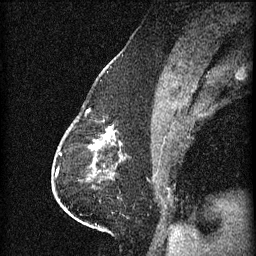
Breast MRI (dynamic contrast-enhanced), one sagittal slice; position 27 of 60 along the scan axis; 3 images stored at this slice position (order not interpretable as contrast timing); 1.5 T; TE 4.2 ms, TR 11 ms; 1.5 mm slice thickness; 256 × 256 image matrix, field of view 180 × 180 mm. Patient: female, 63 years.
Outlined on this slice (semi-automatically segmented with operator editing):
- analysis volume of interest (the breast-tissue region the enhancement analysis was run in; not a lesion): bounding box <90,124,123,153> (left, top, right, bottom; pixels)
- tumour enhancement mask (voxels above the 70 % enhancement threshold inside the analysis volume of interest): <90,128,121,151>